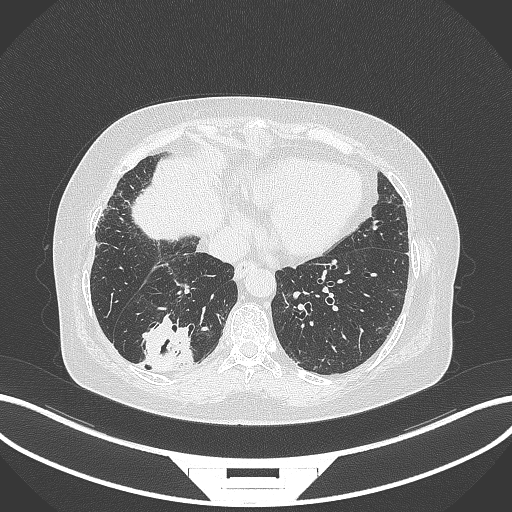
Chest CT, one axial slice. Position 60 of 296 along the scan axis. Reconstruction kernel B70f. 120 kVp. Lung window (W 1500 / L -600 HU). 1 mm slice thickness. 512 × 512 image matrix, field of view 400 × 400 mm. Female patient, age 65 years. From the clinical record (not read from this slice): clinical TNM (as recorded): T2b N1 M0; histopathological grade: G1.
Structures marked on this image (rectangle marked by the reading radiologist):
- lung tumour (recorded histology: adenocarcinoma): bounding box [x1, y1, x2, y2] px = [137, 312, 198, 373]